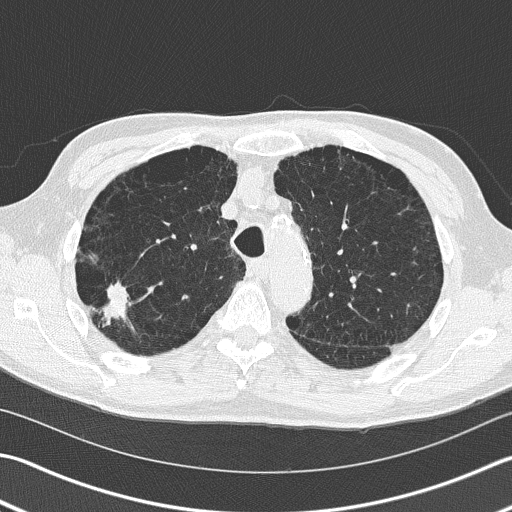
Axial slice from a low-dose chest CT screening exam, first (baseline) screen, lung window (W 1500 / L -600 HU), lung (sharp) reconstruction kernel (B50f), slice 45 of 163 in the series, 512 × 512 image matrix, field of view 346 × 346 mm. Male participant, aged 66 years at enrolment. Current smoker at enrolment.
Expert-annotated lung lesion, bounding box (x1, y1, x2, y2) in pixels: (76, 258, 141, 339). Reader record for this screening exam (exam-level; its link to the box is not recorded): non-calcified nodule or mass ≥4 mm, right upper lobe, 39 × 23 mm, spiculated (stellate) margins, soft tissue attenuation. Official screen result: positive, change unspecified: nodule(s) >= 4 mm or enlarging nodule(s), mass(es), or other non-specific abnormalities suspicious for lung cancer. Participant outcome: lung cancer diagnosed 36 days after this screen — squamous cell carcinoma, NOS, right upper lobe, poorly differentiated (G3), stage IB (AJCC 6th edition), 23 mm at pathology.